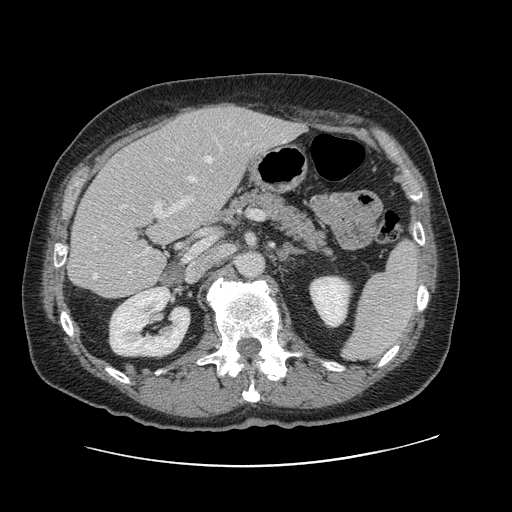
Contrast-enhanced abdominal CT, one axial slice. Soft-tissue window (W 400 / L 40 HU). 512 × 512 image matrix. Male patient, age 71 years. From the clinical record (not read from this slice): diagnosis: colorectal cancer liver metastases, imaged before liver resection; multiple liver metastases: no; largest metastasis: 3.3 cm; chemotherapy before resection: no.
Outlined on this slice (outlined manually by an expert reader):
- hepatic veins: box from (x=93, y=156) to (x=227, y=279) px
- liver: (x=70, y=105)–(x=303, y=298)
- planned liver remnant (the part of the liver to remain after resection): (x=70, y=143)–(x=202, y=298)
- portal vein (with intrahepatic branches): (x=95, y=143)–(x=248, y=250)